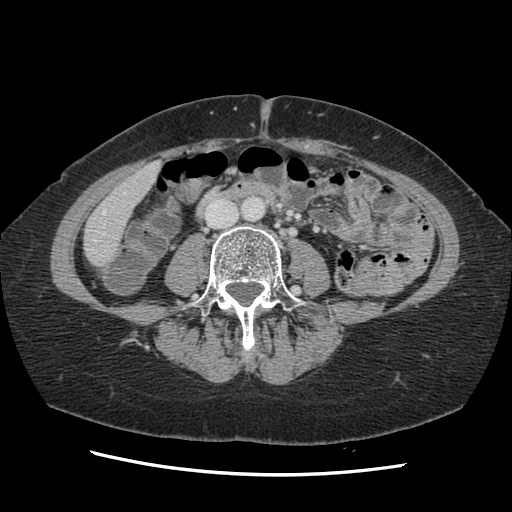
Contrast-enhanced abdominal CT, one axial slice; slice 24 of 141 in the series (ordered by position); 120 kVp; soft-tissue window (W 400 / L 40 HU); 512 × 512 image matrix, field of view 330 × 330 mm. Female patient, age 61 years. Case-level facts recorded for this patient, not image findings: diagnosis: colorectal cancer liver metastases, imaged before liver resection; multiple liver metastases: no; largest metastasis: 2.4 cm; disease in both lobes: no.
Structures marked on this image (expert manual segmentation):
- hepatic veins: bounding box [x1, y1, x2, y2] px = [94, 210, 106, 242]
- liver: [84, 164, 160, 265]
- planned liver remnant (the part of the liver to remain after resection): [84, 165, 160, 265]